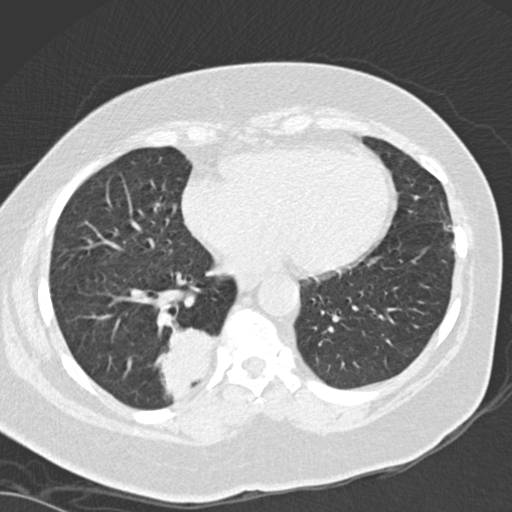
Low-dose screening chest CT, one axial slice; slice 60 of 162 in the series (ordered by position); reconstruction kernel B30f; 120 kVp; lung window (W 1500 / L -600 HU); 512 × 512 image matrix, field of view 328 × 328 mm.
Outlined on this slice (outlined manually by an expert reader):
- lesion 1 (tumor, lower lobe of right lung): box from (x=155, y=327) to (x=216, y=401) px